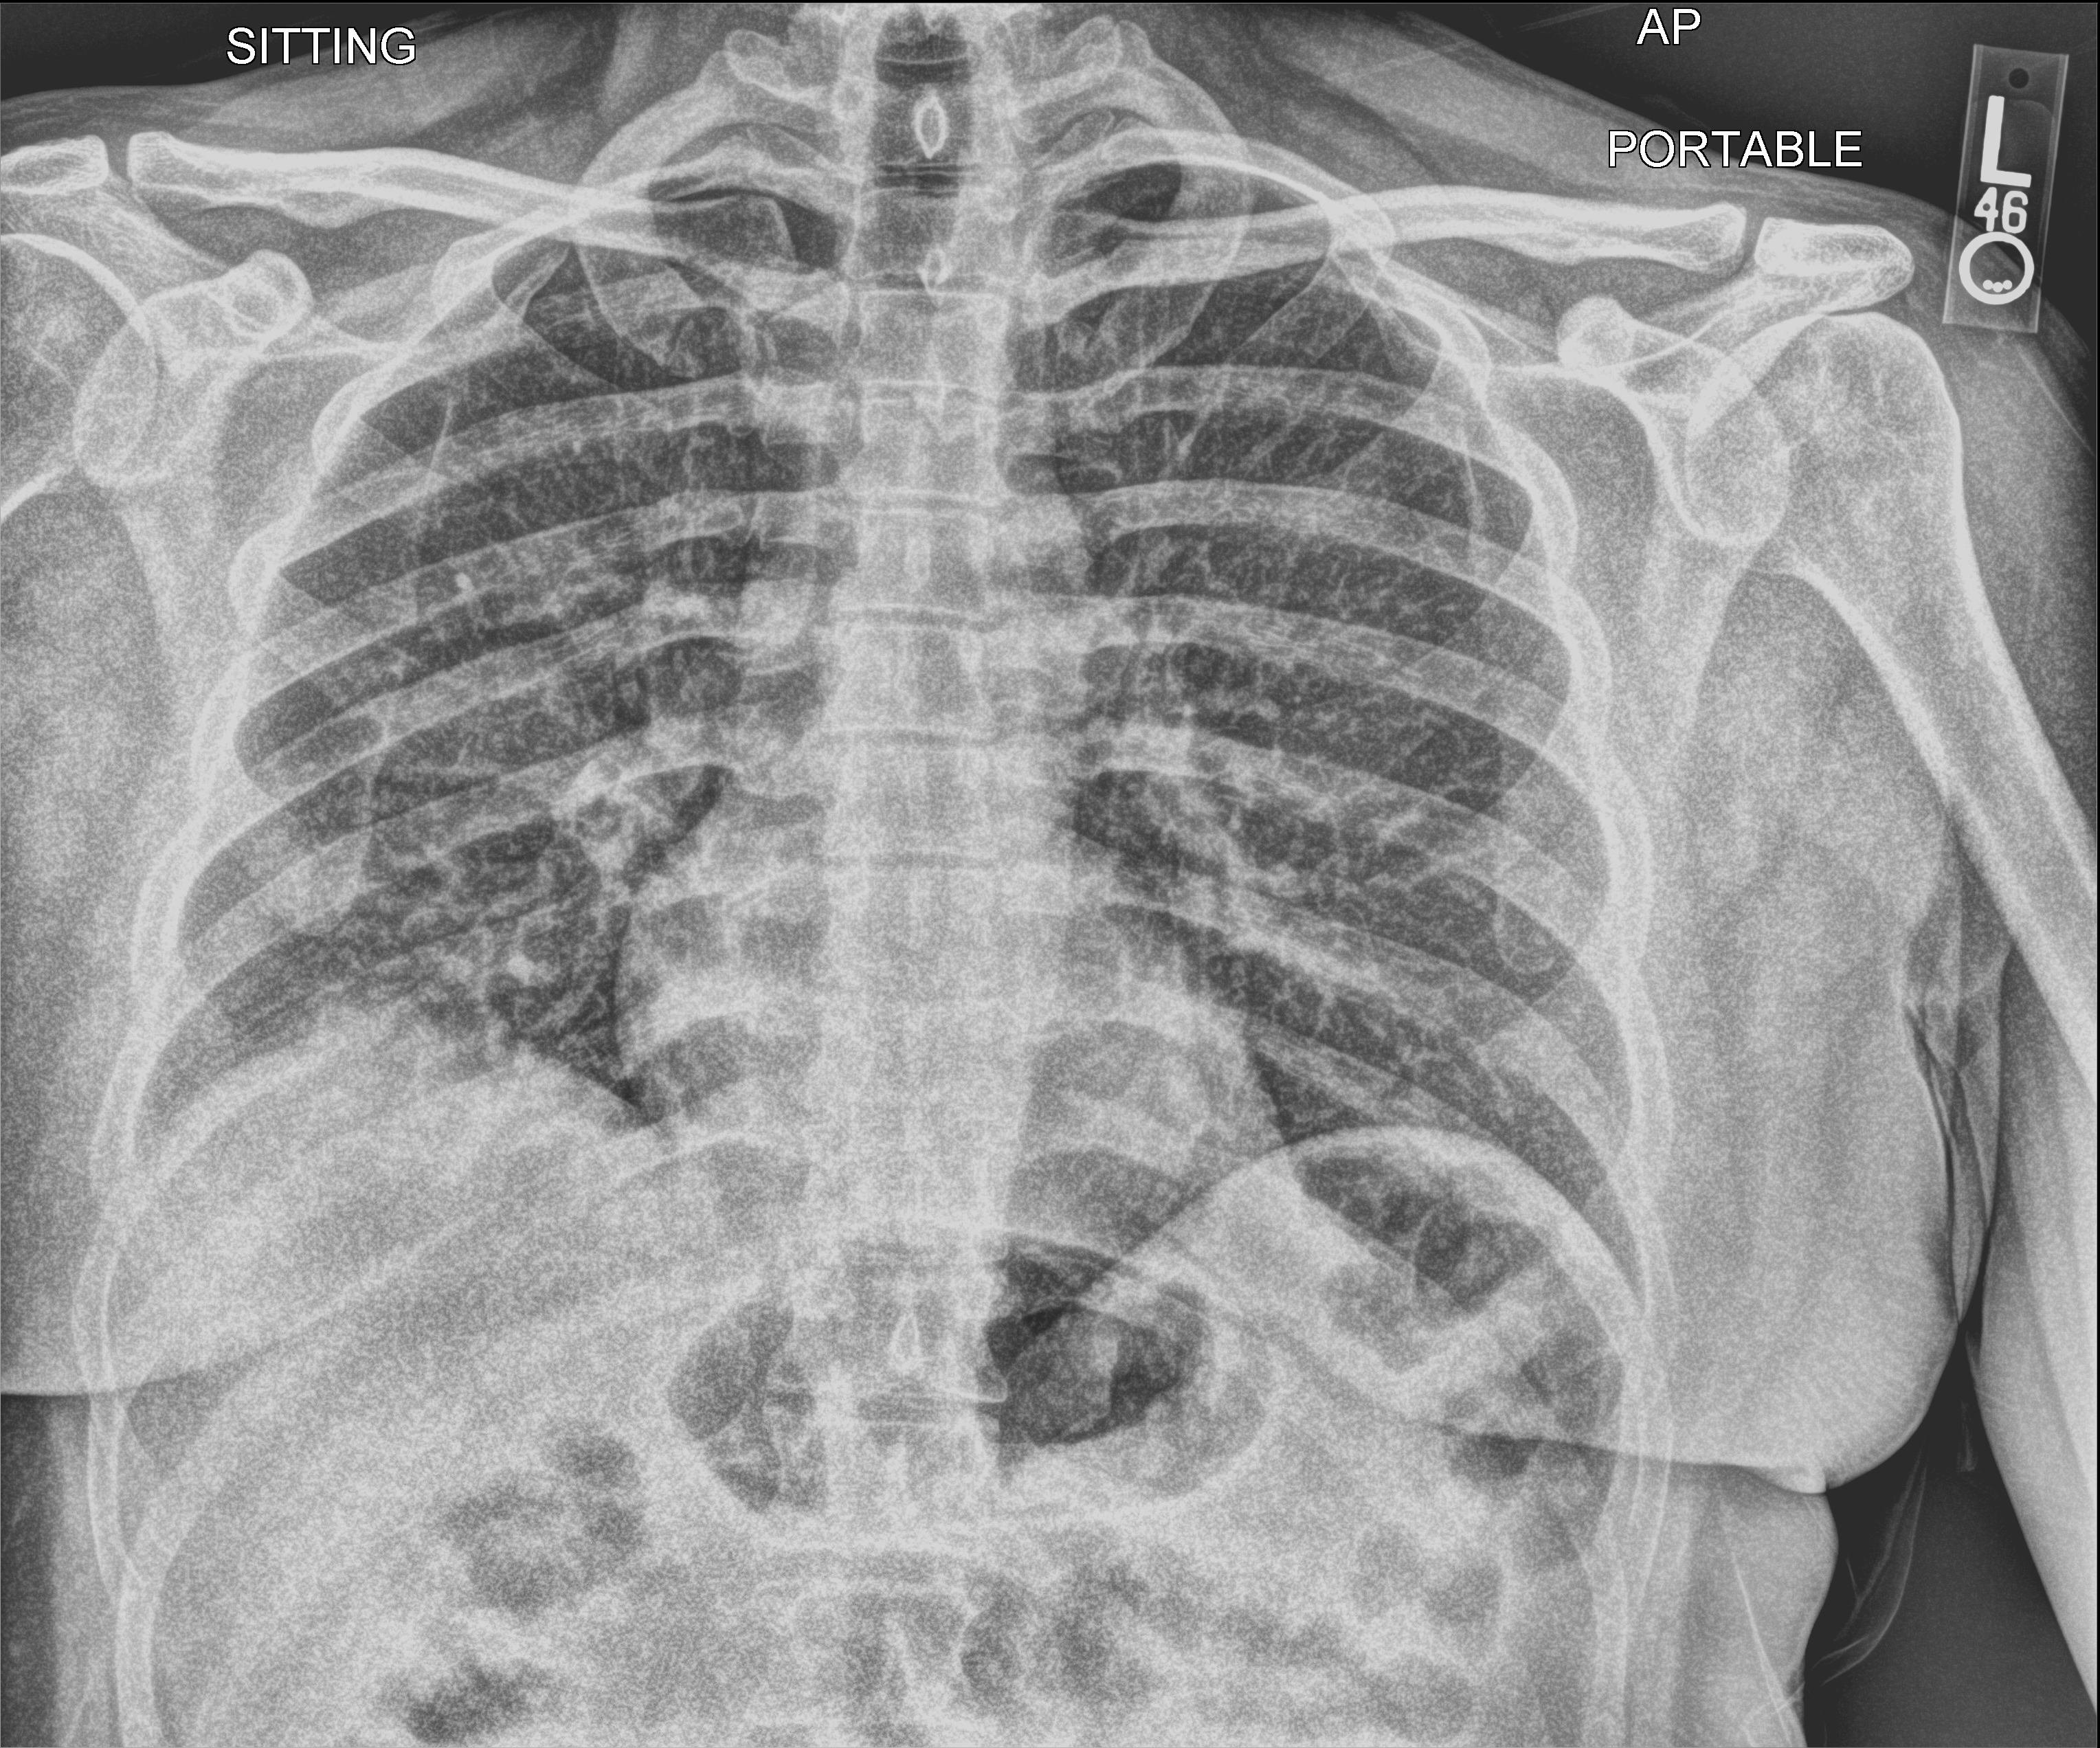
Chest X-ray (portable); anteroposterior (AP) projection. Patient hospitalised with COVID-19; male, aged 18–59 years.
Hospital-stay facts (about this admission, not read from this image; timing relative to this image not recorded): admitted to intensive care during this hospital stay: no; other chronic lung disease (admission record): no; mechanically ventilated during this hospital stay: no.